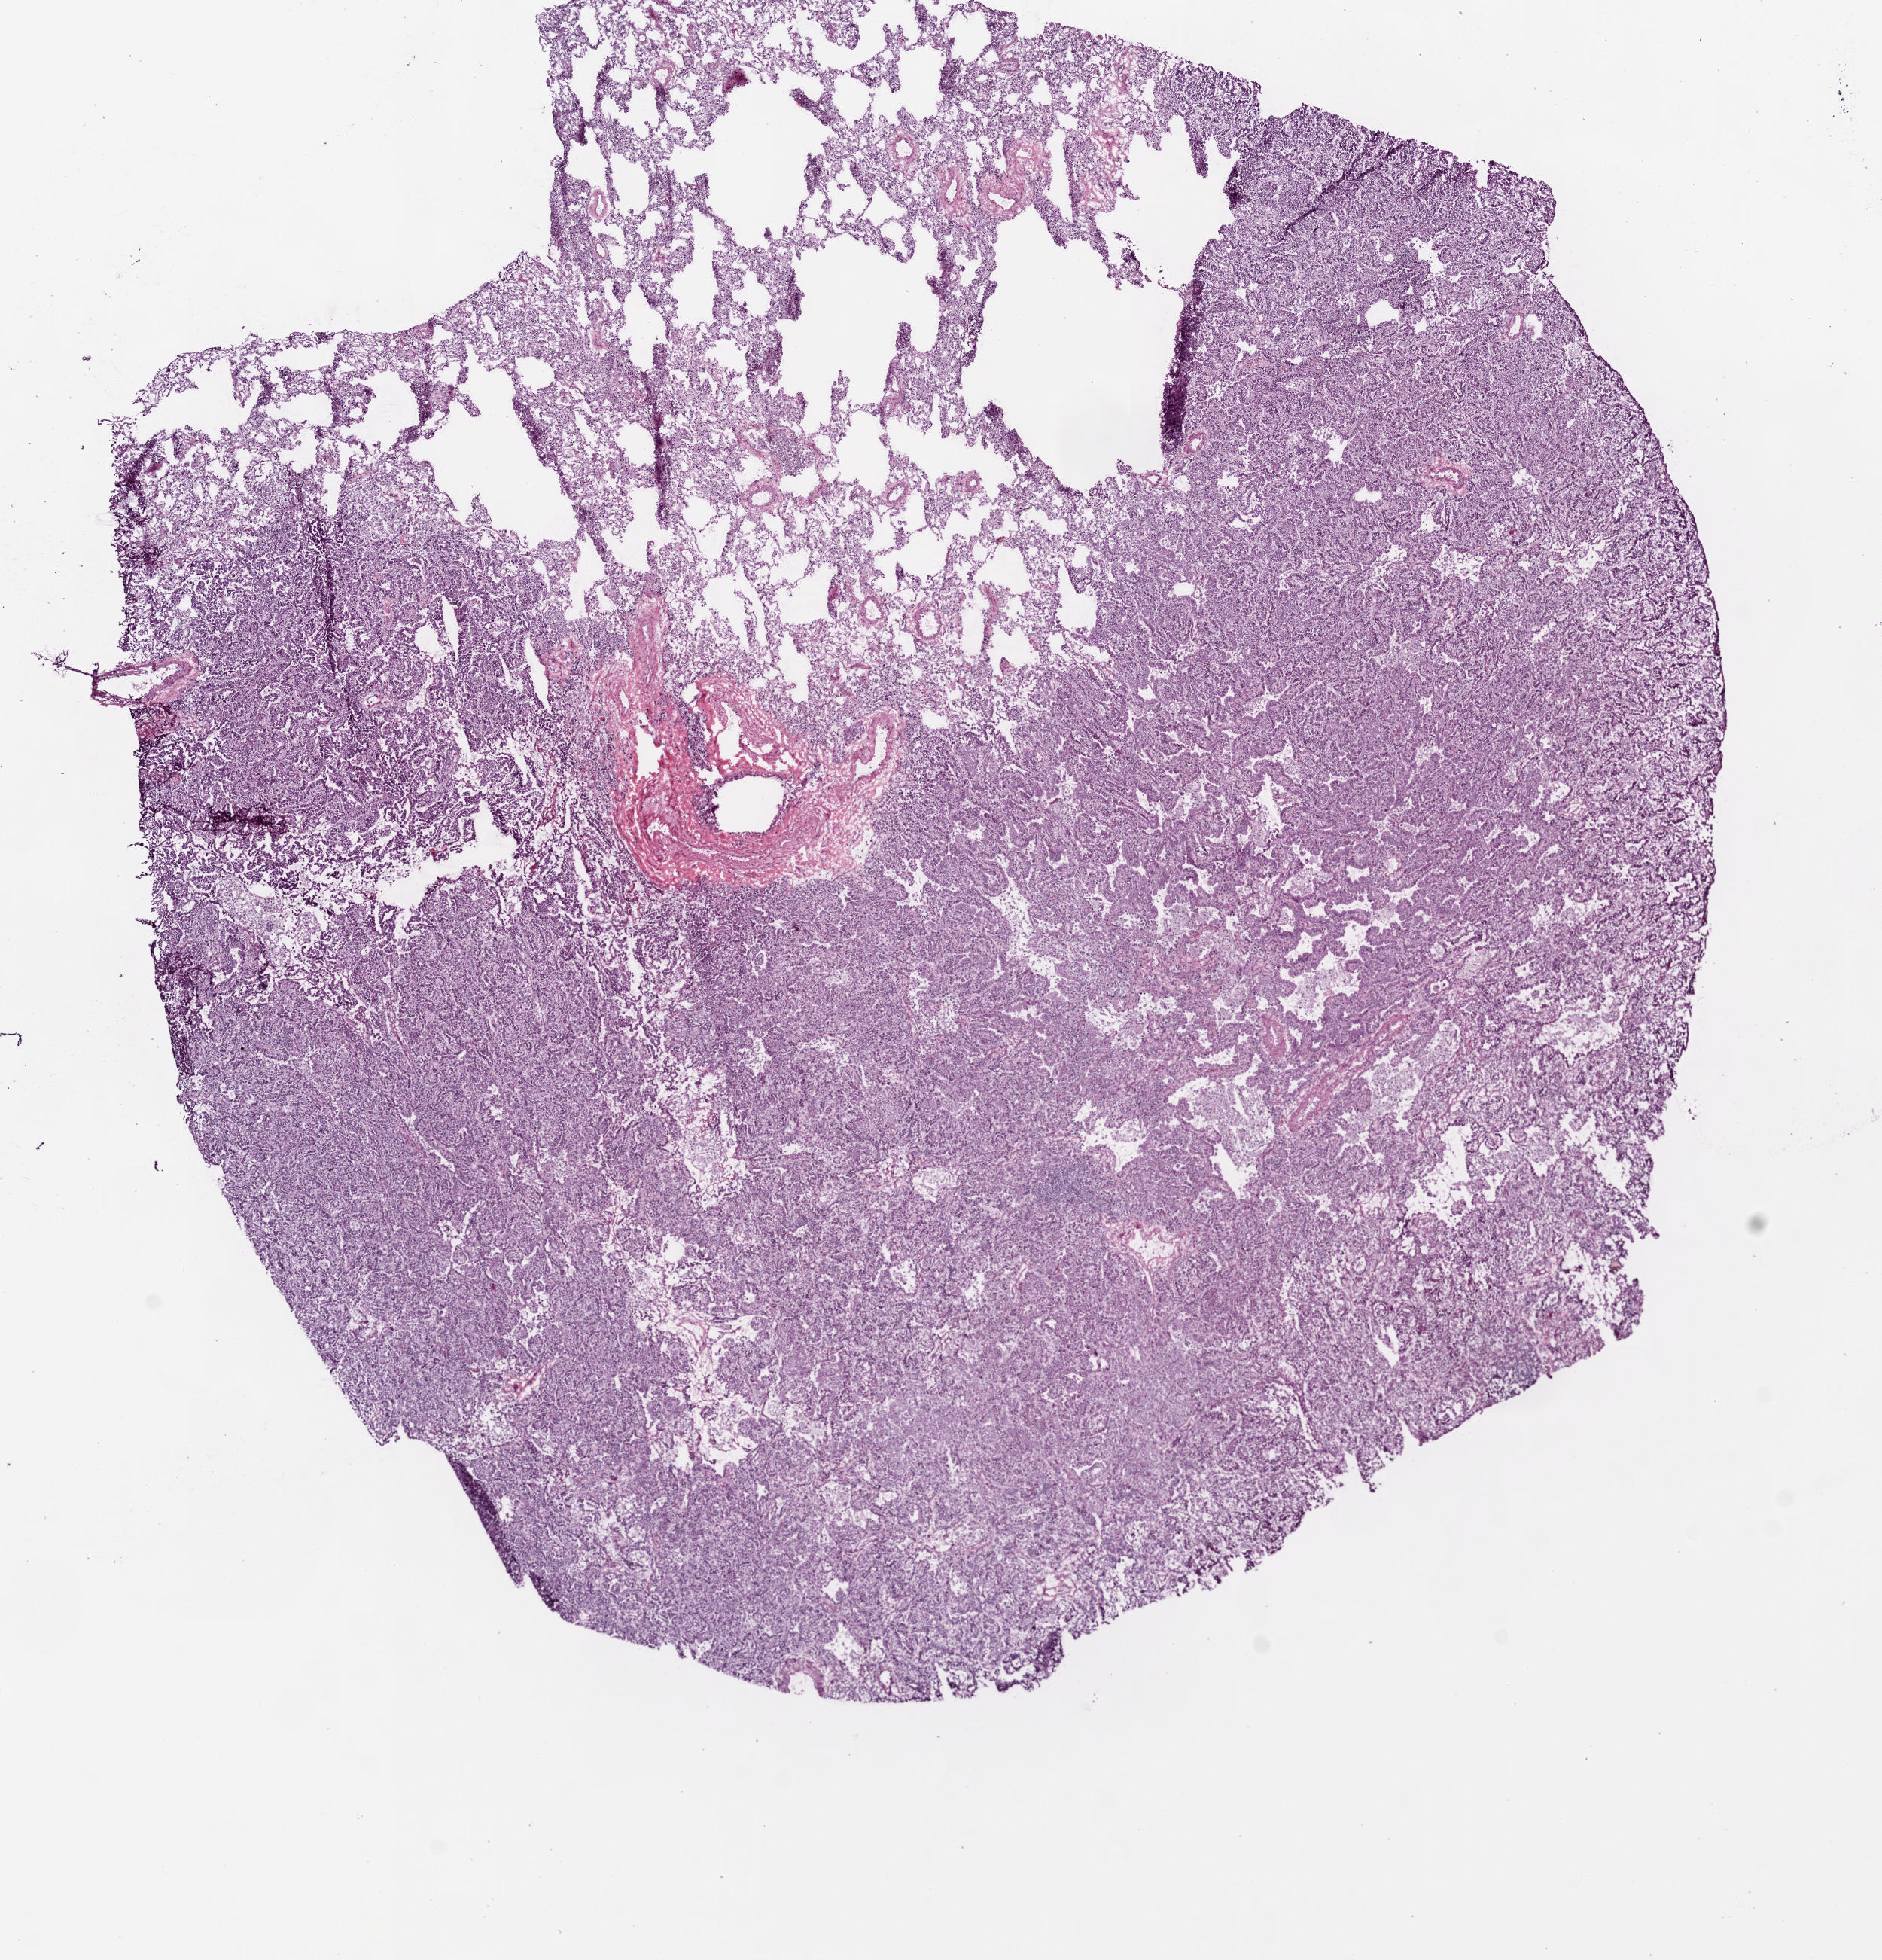
H&E whole-slide image — a low-resolution overview of the entire scanned area, about 10.0 x 10.4 mm, frozen section, primary tumour sample from the lung. Male patient; age at initial diagnosis 66 years.
Diagnosis: Adenocarcinoma with mixed subtypes (lower lobe, lung).